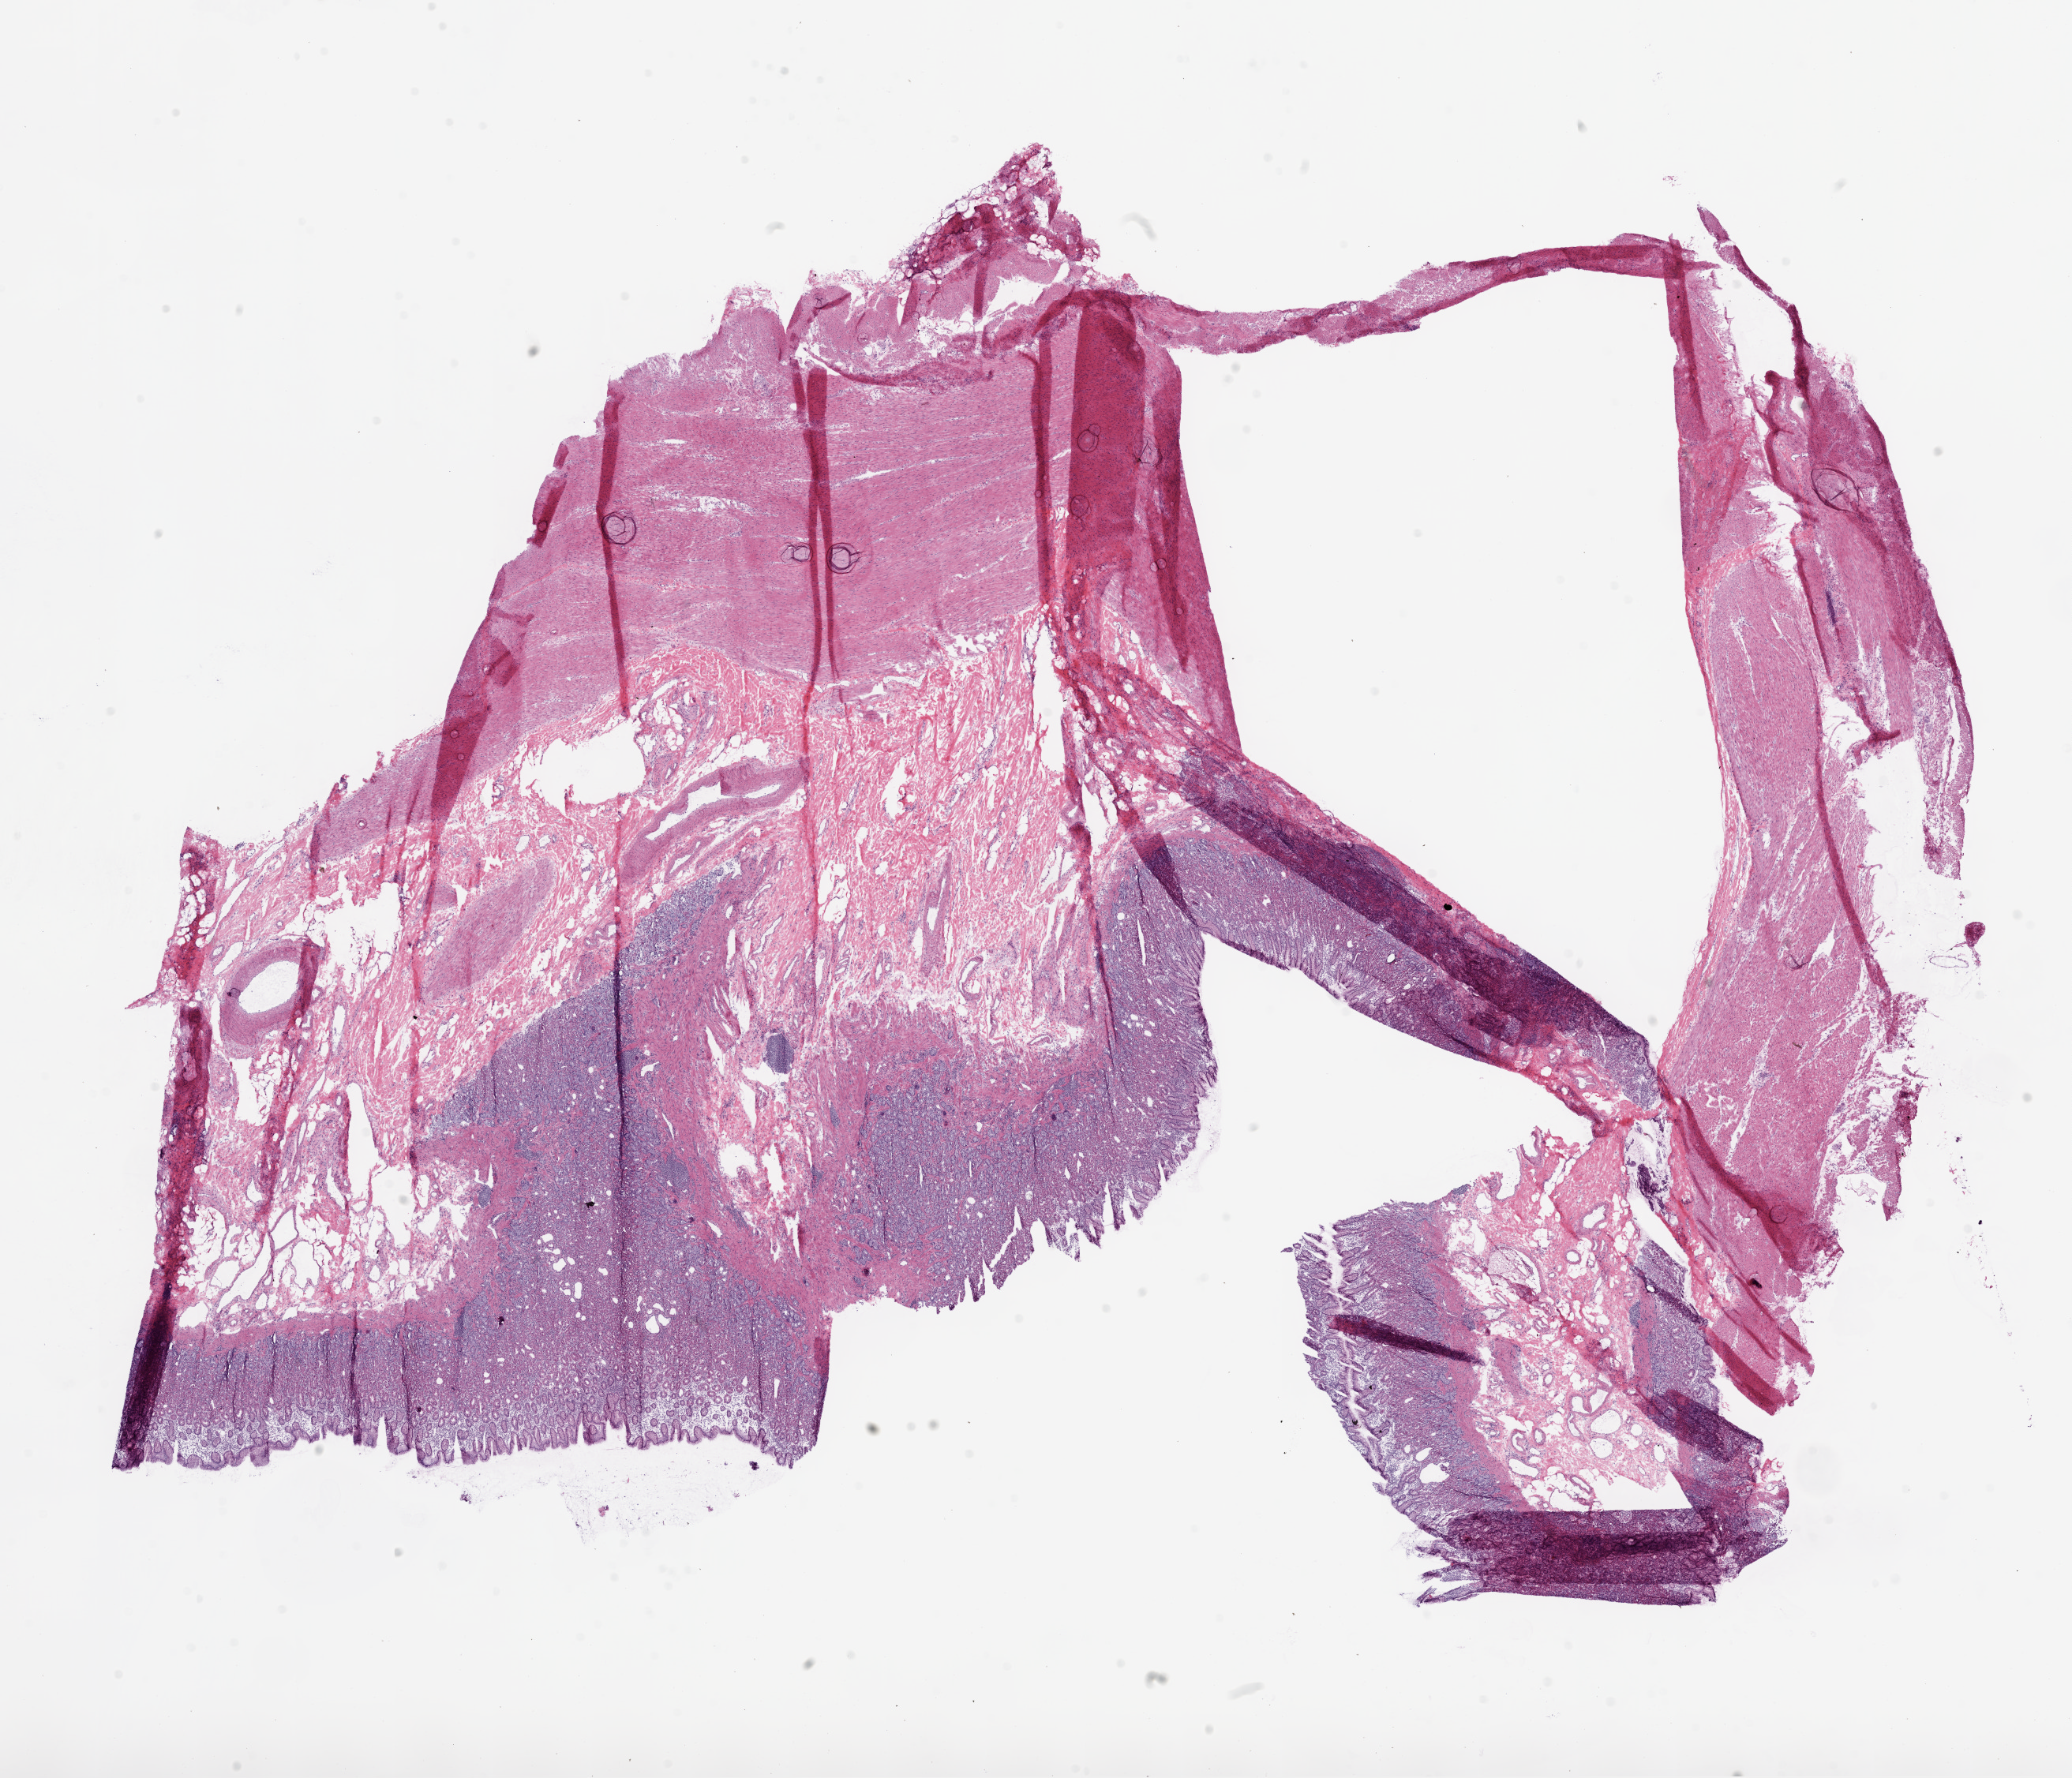
Hematoxylin and eosin (H&E) stained whole-slide image — shown as a low-resolution overview of the whole scanned area (about 21.1 x 18.1 mm). Frozen section from the bottom of the tissue portion. Solid tissue normal (non-tumour tissue) sample from the stomach. Female patient; age at initial diagnosis 74 years.
This section: solid tissue normal sample (biorepository sample class). Patient diagnosis: Adenocarcinoma, NOS.